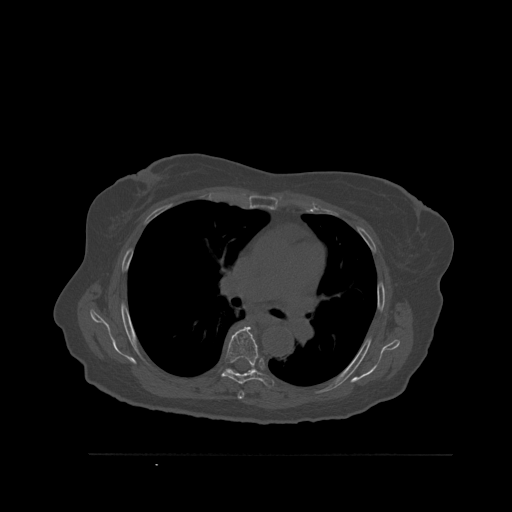
CT including the spine, one axial slice; bone window (W 1800 / L 400 HU); 1.5 mm slice thickness; 512 × 512 image matrix, field of view 470 × 470 mm. Female patient, age 73 years. Case-level facts recorded for this patient, not image findings: primary cancer: breast.
Structures marked on this image (semi-automatically segmented with operator editing):
- T5 vertebra: bounding box [x1, y1, x2, y2] px = [237, 391, 244, 399]
- T6 vertebra: [222, 327, 274, 388]